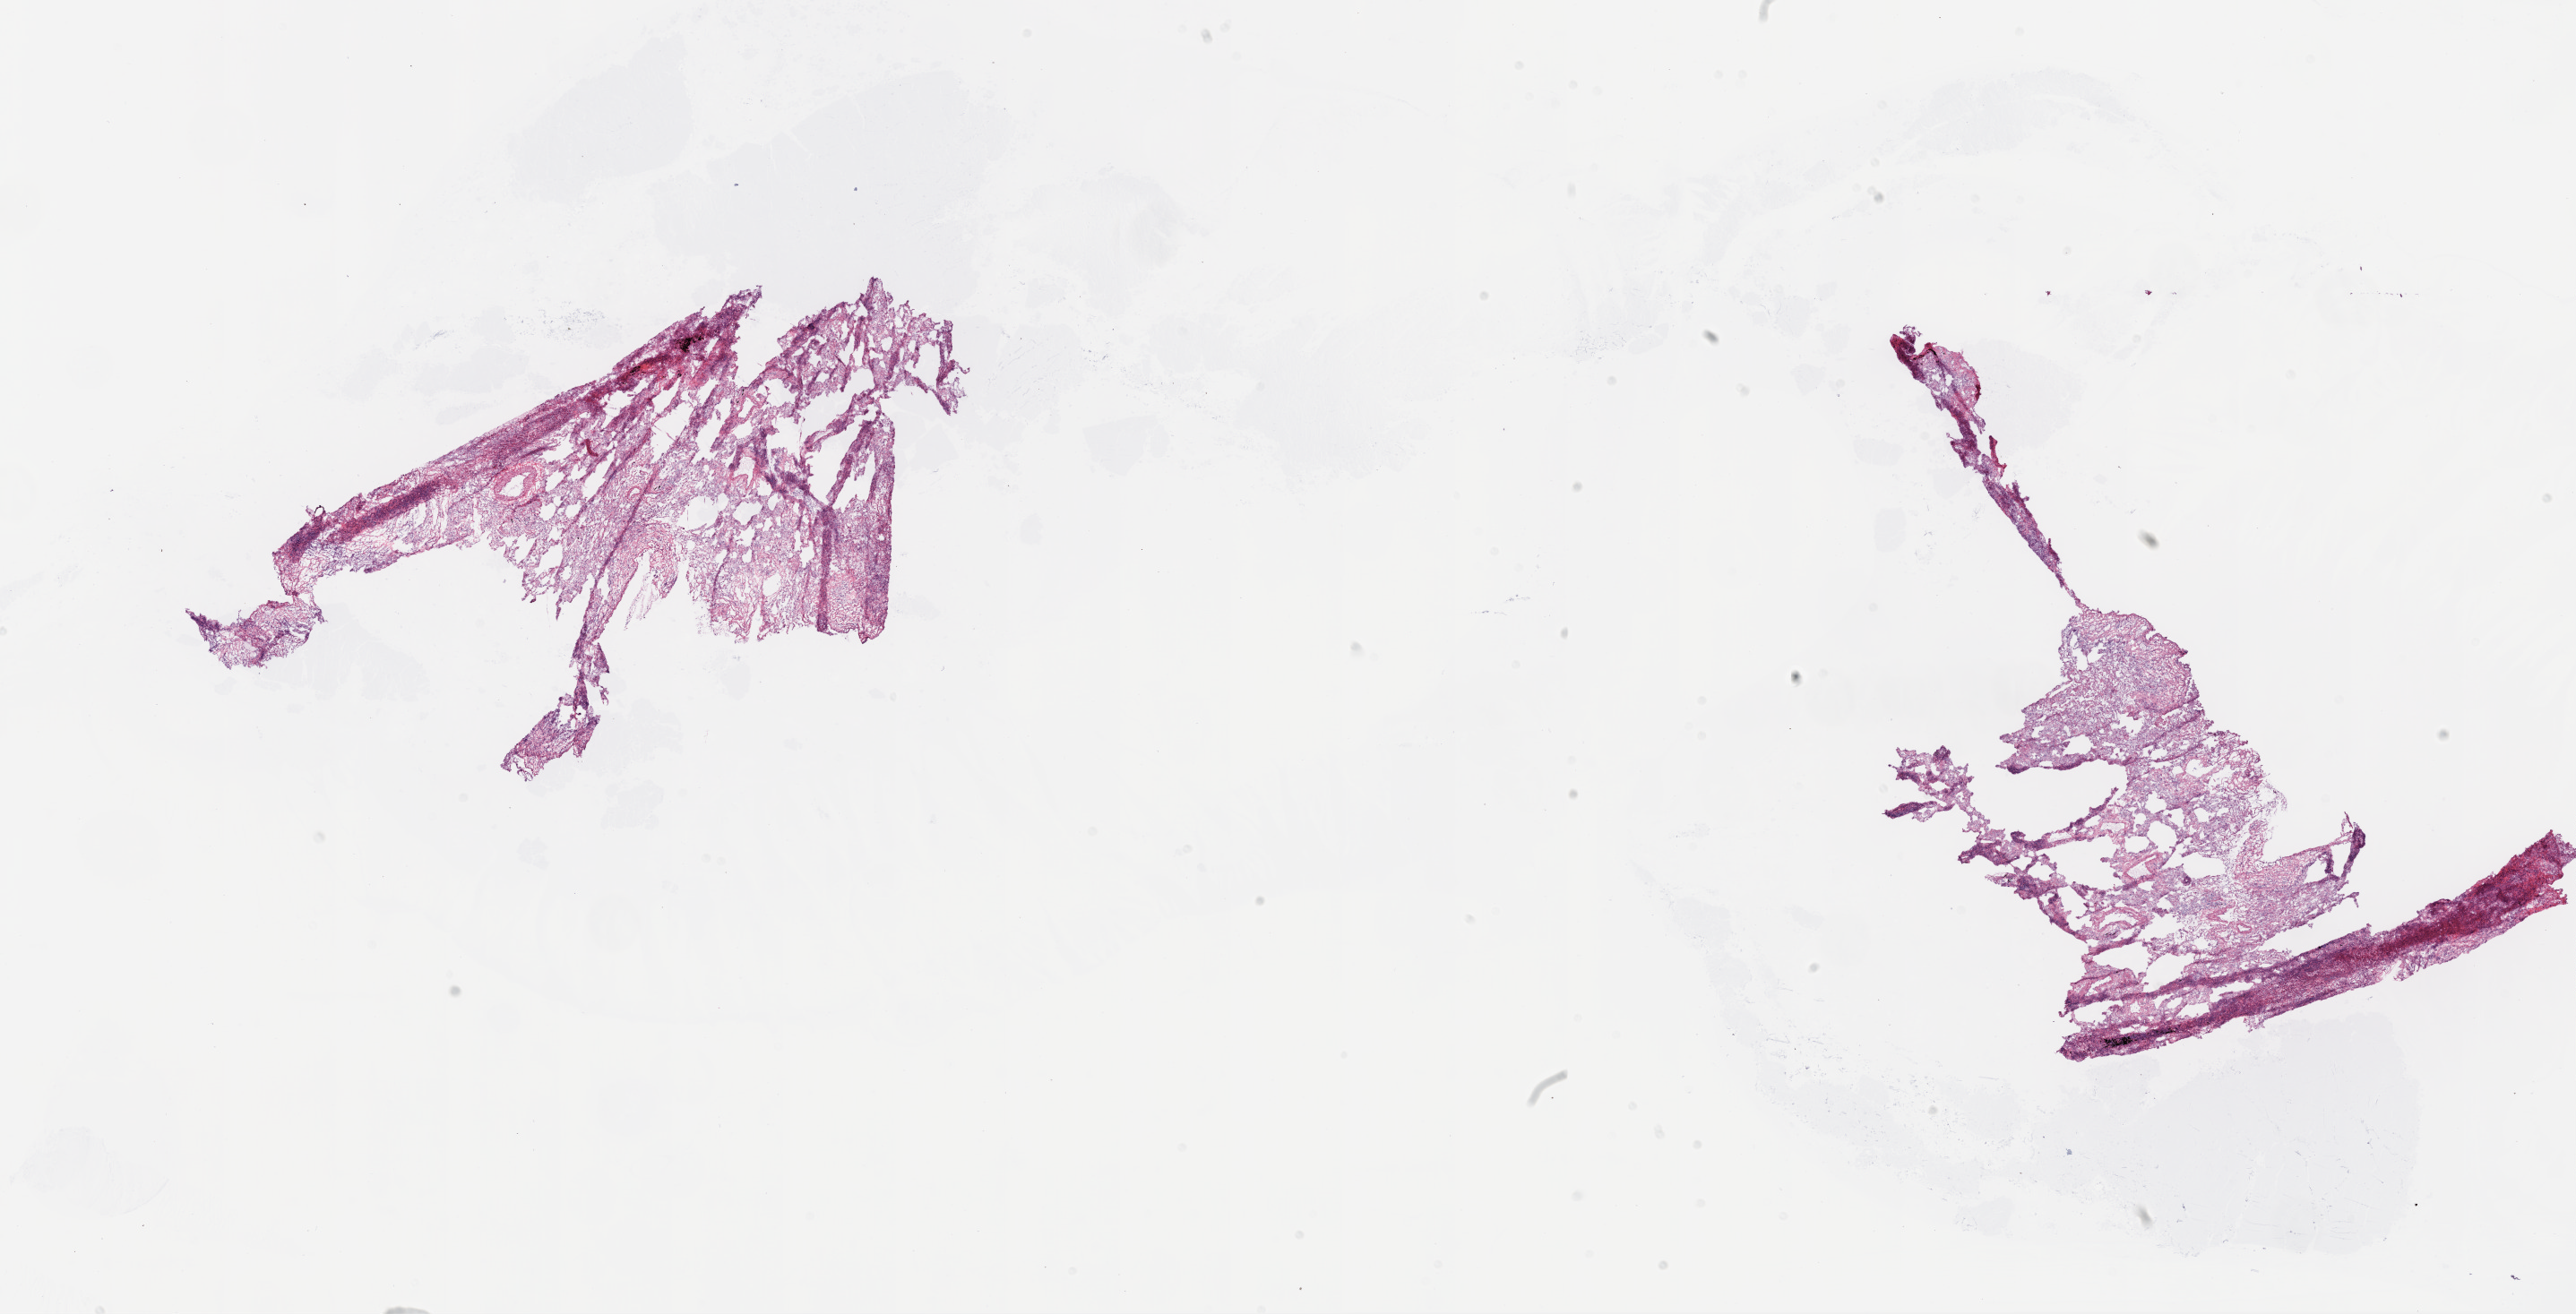
H&E-stained whole-slide image, a low-resolution overview of the entire scanned area, about 23.1 x 11.8 mm; frozen section from the top of the tissue portion; sample: solid tissue normal (non-tumour tissue), lung. Female, age 55 years at initial diagnosis.
This section: solid tissue normal (non-tumour) sample from the same patient. Patient diagnosis: Squamous cell carcinoma, NOS (lower lobe, lung).